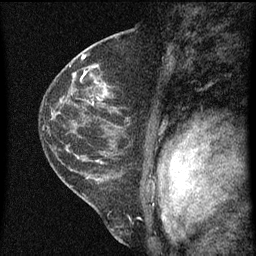
Breast MRI (dynamic contrast-enhanced), one sagittal slice; dynamic contrast-enhanced series, image 2 of 3 at this slice position (ordered by acquisition); 1.5 T; TE 4.2 ms, TR 8 ms; 256 × 256 image matrix, field of view 180 × 180 mm. Female patient, age 48 years.
Annotated regions visible in this slice (semi-automatically segmented with operator editing):
- analysis volume of interest (the breast-tissue region the enhancement analysis was run in; not a lesion): bounding box [x1, y1, x2, y2] px = [82, 68, 120, 125]
- tumour enhancement mask (voxels above the 70 % enhancement threshold inside the analysis volume of interest): [82, 72, 105, 99]